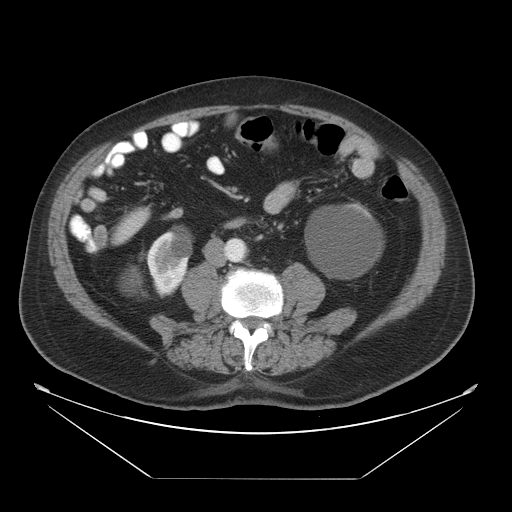
Contrast-enhanced abdominal CT, one axial slice. Slice 7 of 45 in the series (ordered by position). Intravenous contrast given. Soft-tissue window (W 400 / L 40 HU). 5 mm slice thickness. 512 × 512 image matrix, field of view 463 × 463 mm. Male patient, age 87 years. From the clinical record (not read from this slice): diagnosis: colorectal cancer liver metastases, imaged before liver resection; multiple liver metastases: no; largest metastasis: 4.5 cm; disease in both lobes: yes.
Annotated regions visible in this slice (outlined manually by an expert reader):
- liver: box from (x=114, y=208) to (x=145, y=241) px